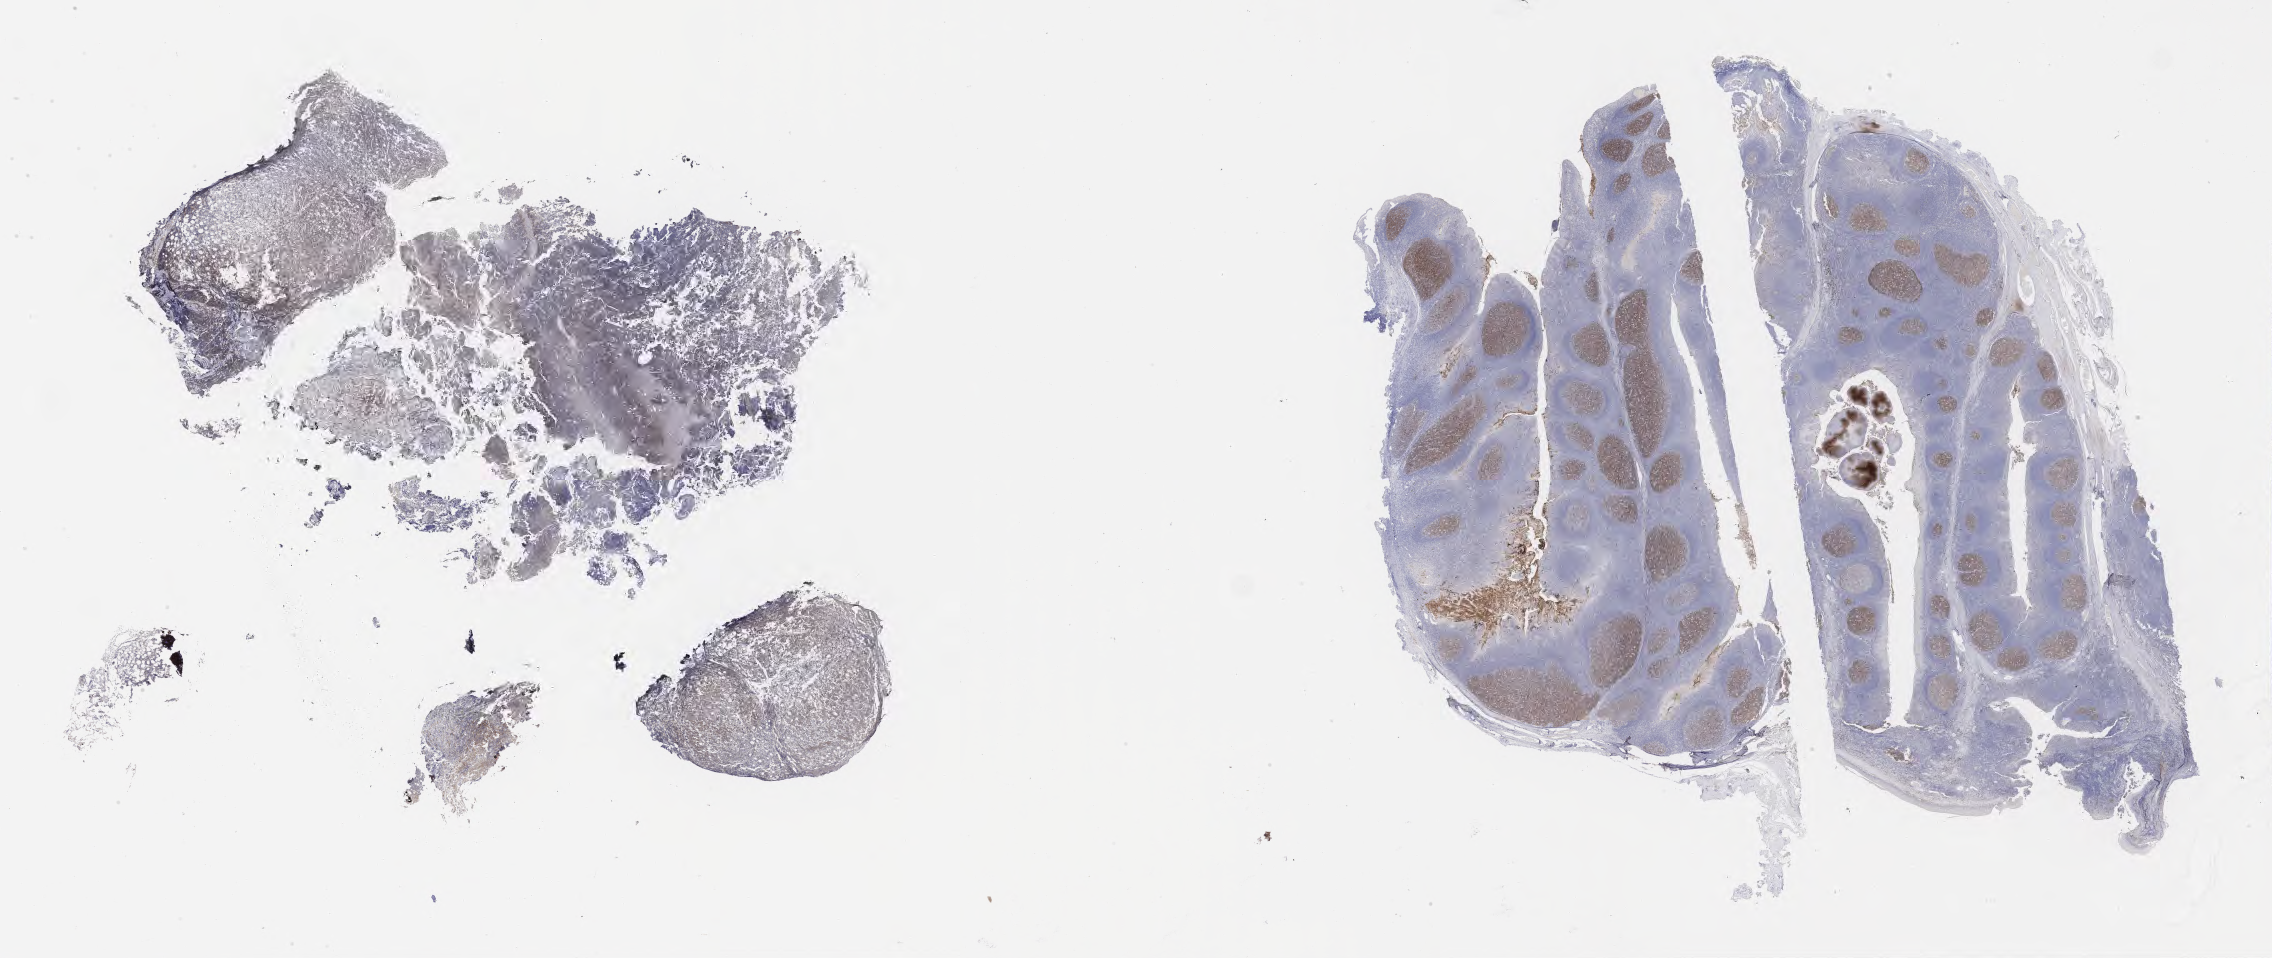
Immunohistochemistry (IHC) whole-slide image stained for CD10 — a low-resolution overview of the entire scanned area, about 36.7 x 15.5 mm. Tumor tissue. Patient: male, age 23 years.
Diagnosis: Burkitt lymphoma, NOS.